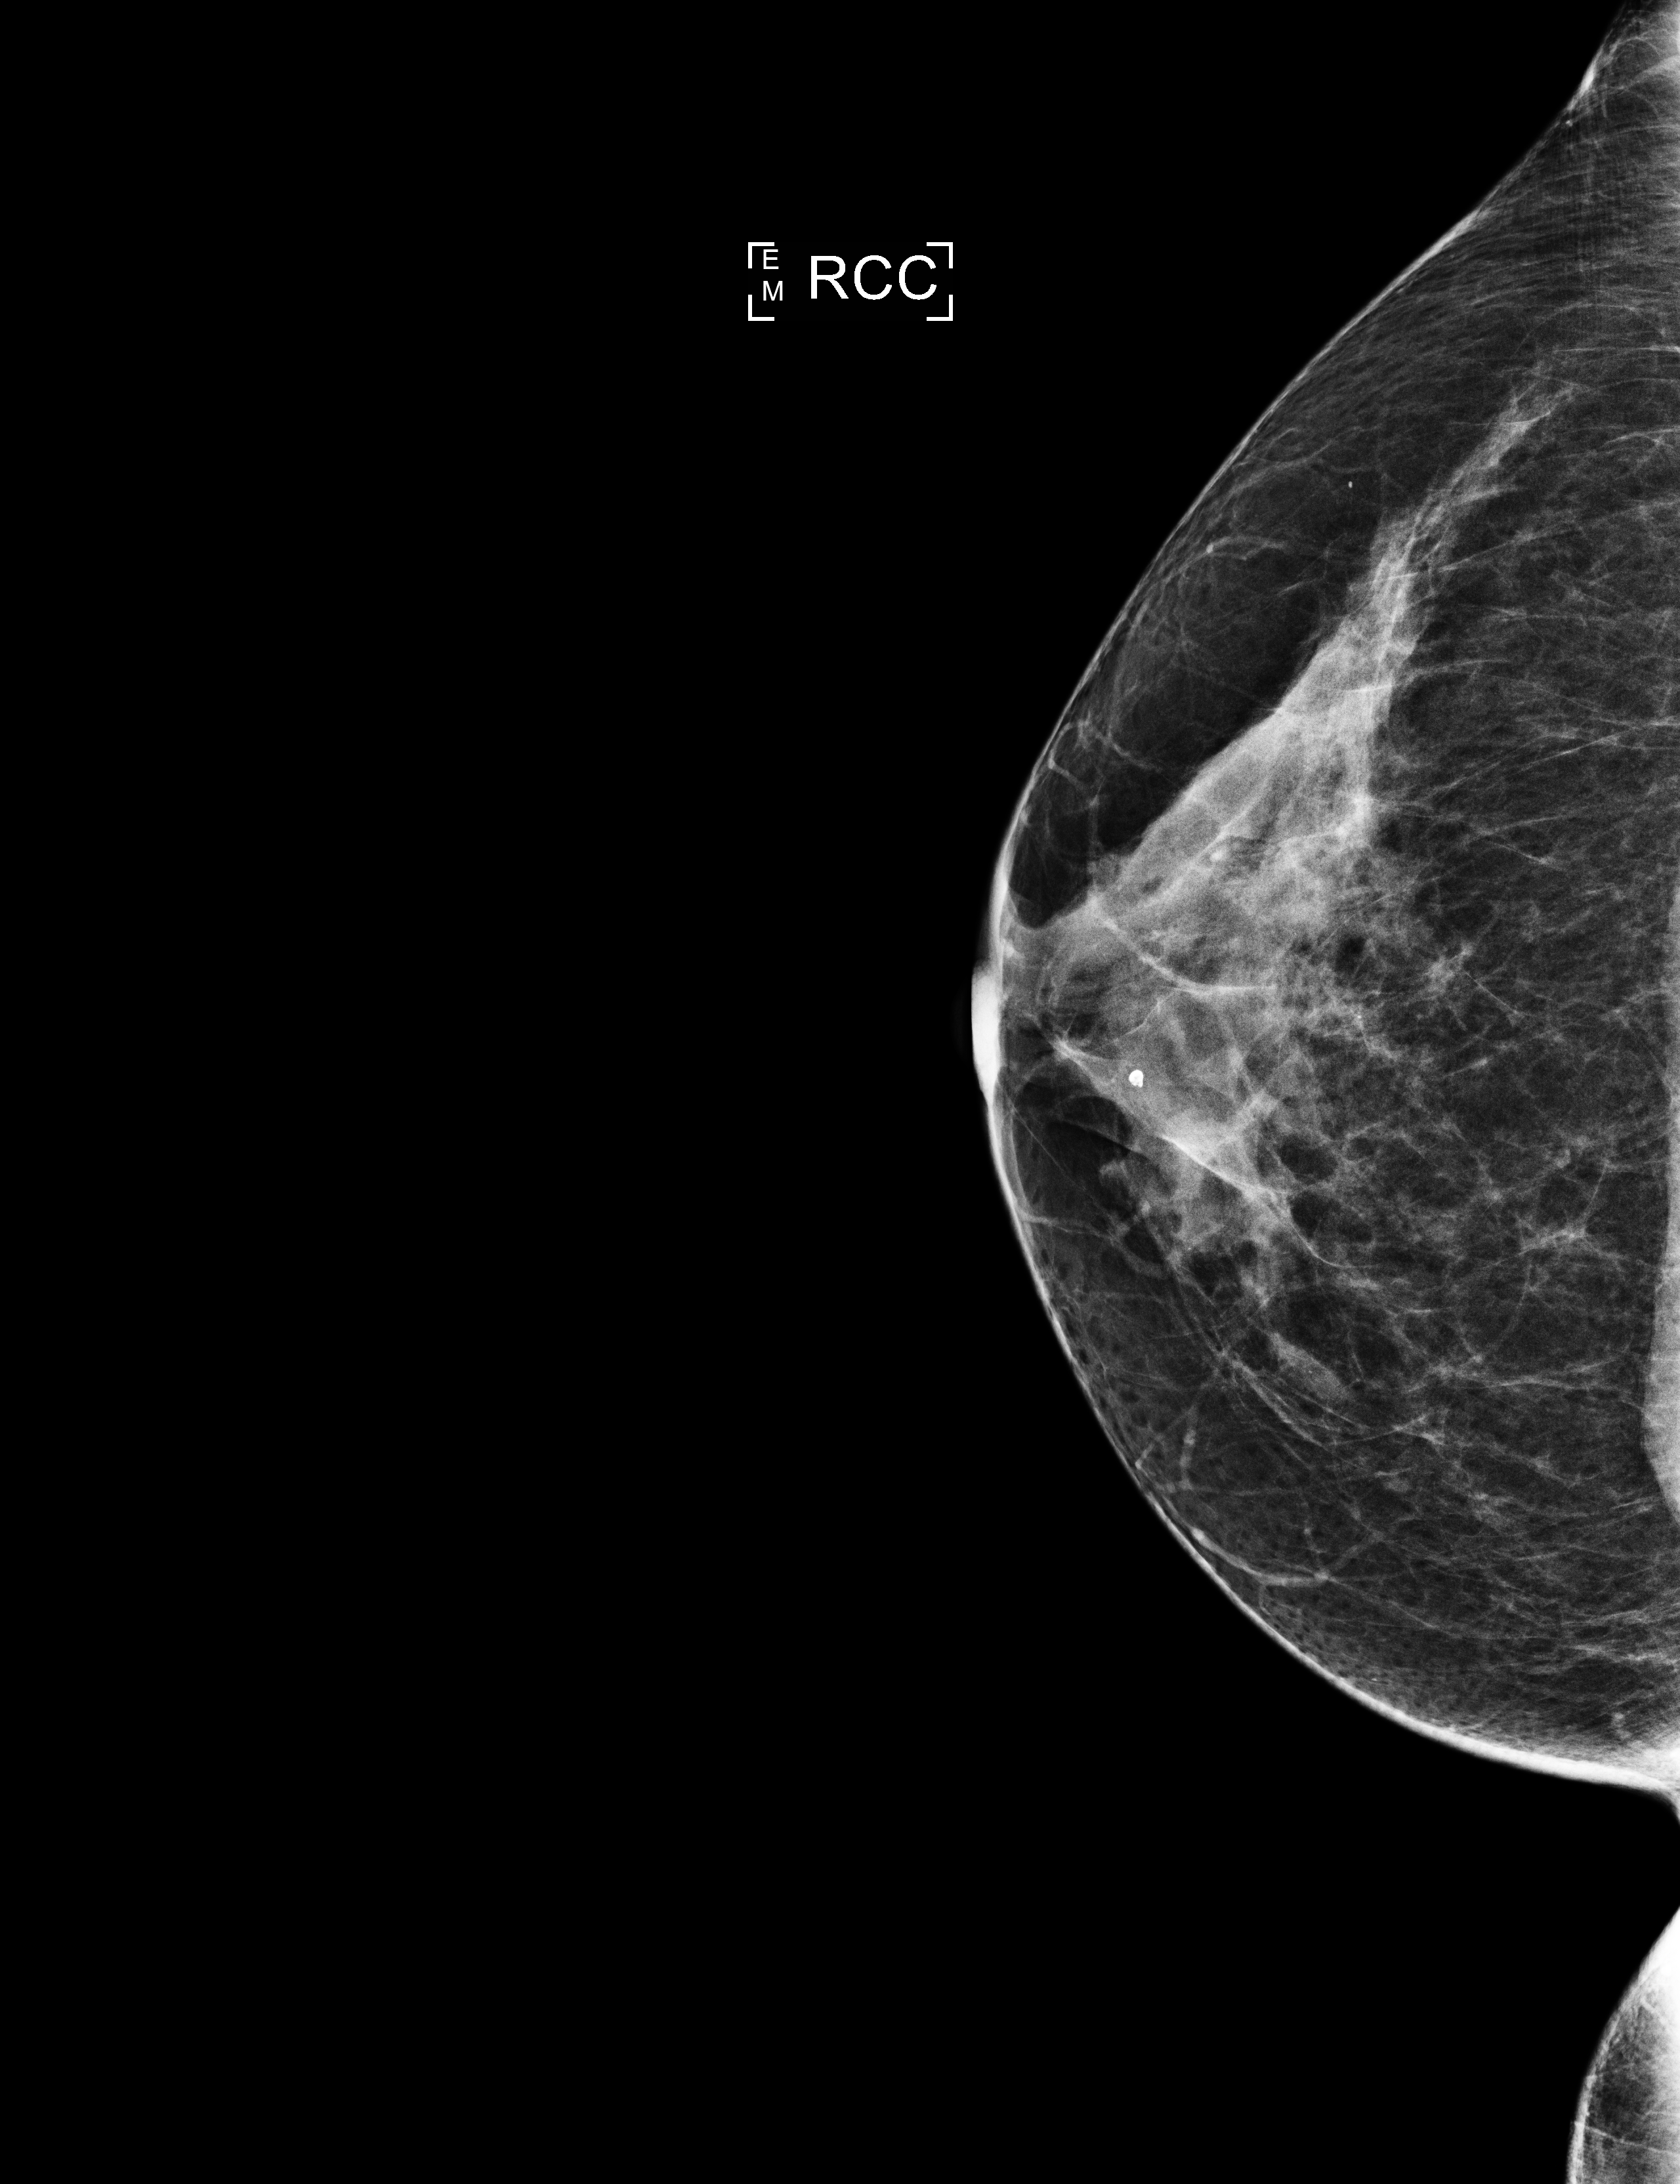
Full-field digital mammogram (FFDM), right breast, craniocaudal (CC) view, screening examination. Patient: female, 56 years.
Breast density at the screening exam (both breasts): heterogeneously dense (BI-RADS density category c). Final BI-RADS category for the screening round (tomosynthesis exam, both breasts): category 2. Recall: no recall after this screen.